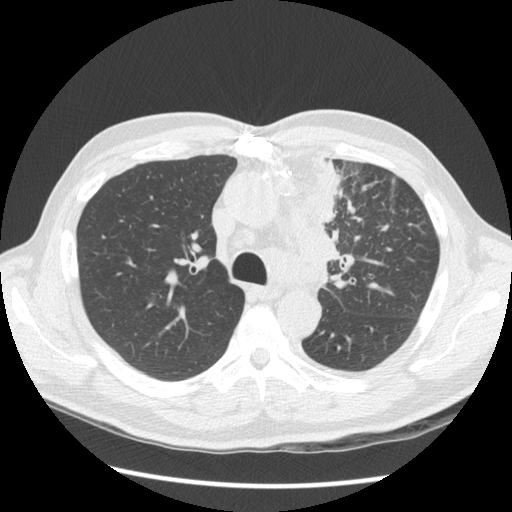
Low-dose screening chest CT, one axial slice. Slice 95 of 136 in the series (ordered by position). Reconstruction kernel STANDARD. 120 kVp. Lung window (W 1500 / L -600 HU). 512 × 512 image matrix, field of view 360 × 360 mm.
Annotated regions visible in this slice (manually delineated by an expert):
- lesion 1 (tumor, upper lobe of left lung): box from (x=303, y=154) to (x=340, y=296) px